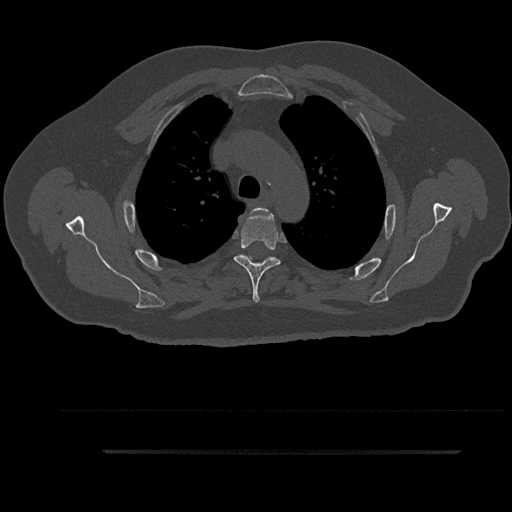
CT including the spine, one axial slice; slice 671 of 797 in the series (ordered by position); bone window (W 1800 / L 400 HU); 0.5 mm slice thickness; 512 × 512 image matrix, field of view 432 × 432 mm. Male patient, age 63 years. Case-level facts recorded for this patient, not image findings: primary cancer: renal; vertebrae with lytic lesions (as recorded): T8.
Structures marked on this image (semi-automatic segmentation, software-assisted and operator-edited):
- T3 vertebra: bounding box (x1, y1, x2, y2) in pixels: (246, 208, 273, 265)
- T4 vertebra: (234, 209, 281, 302)